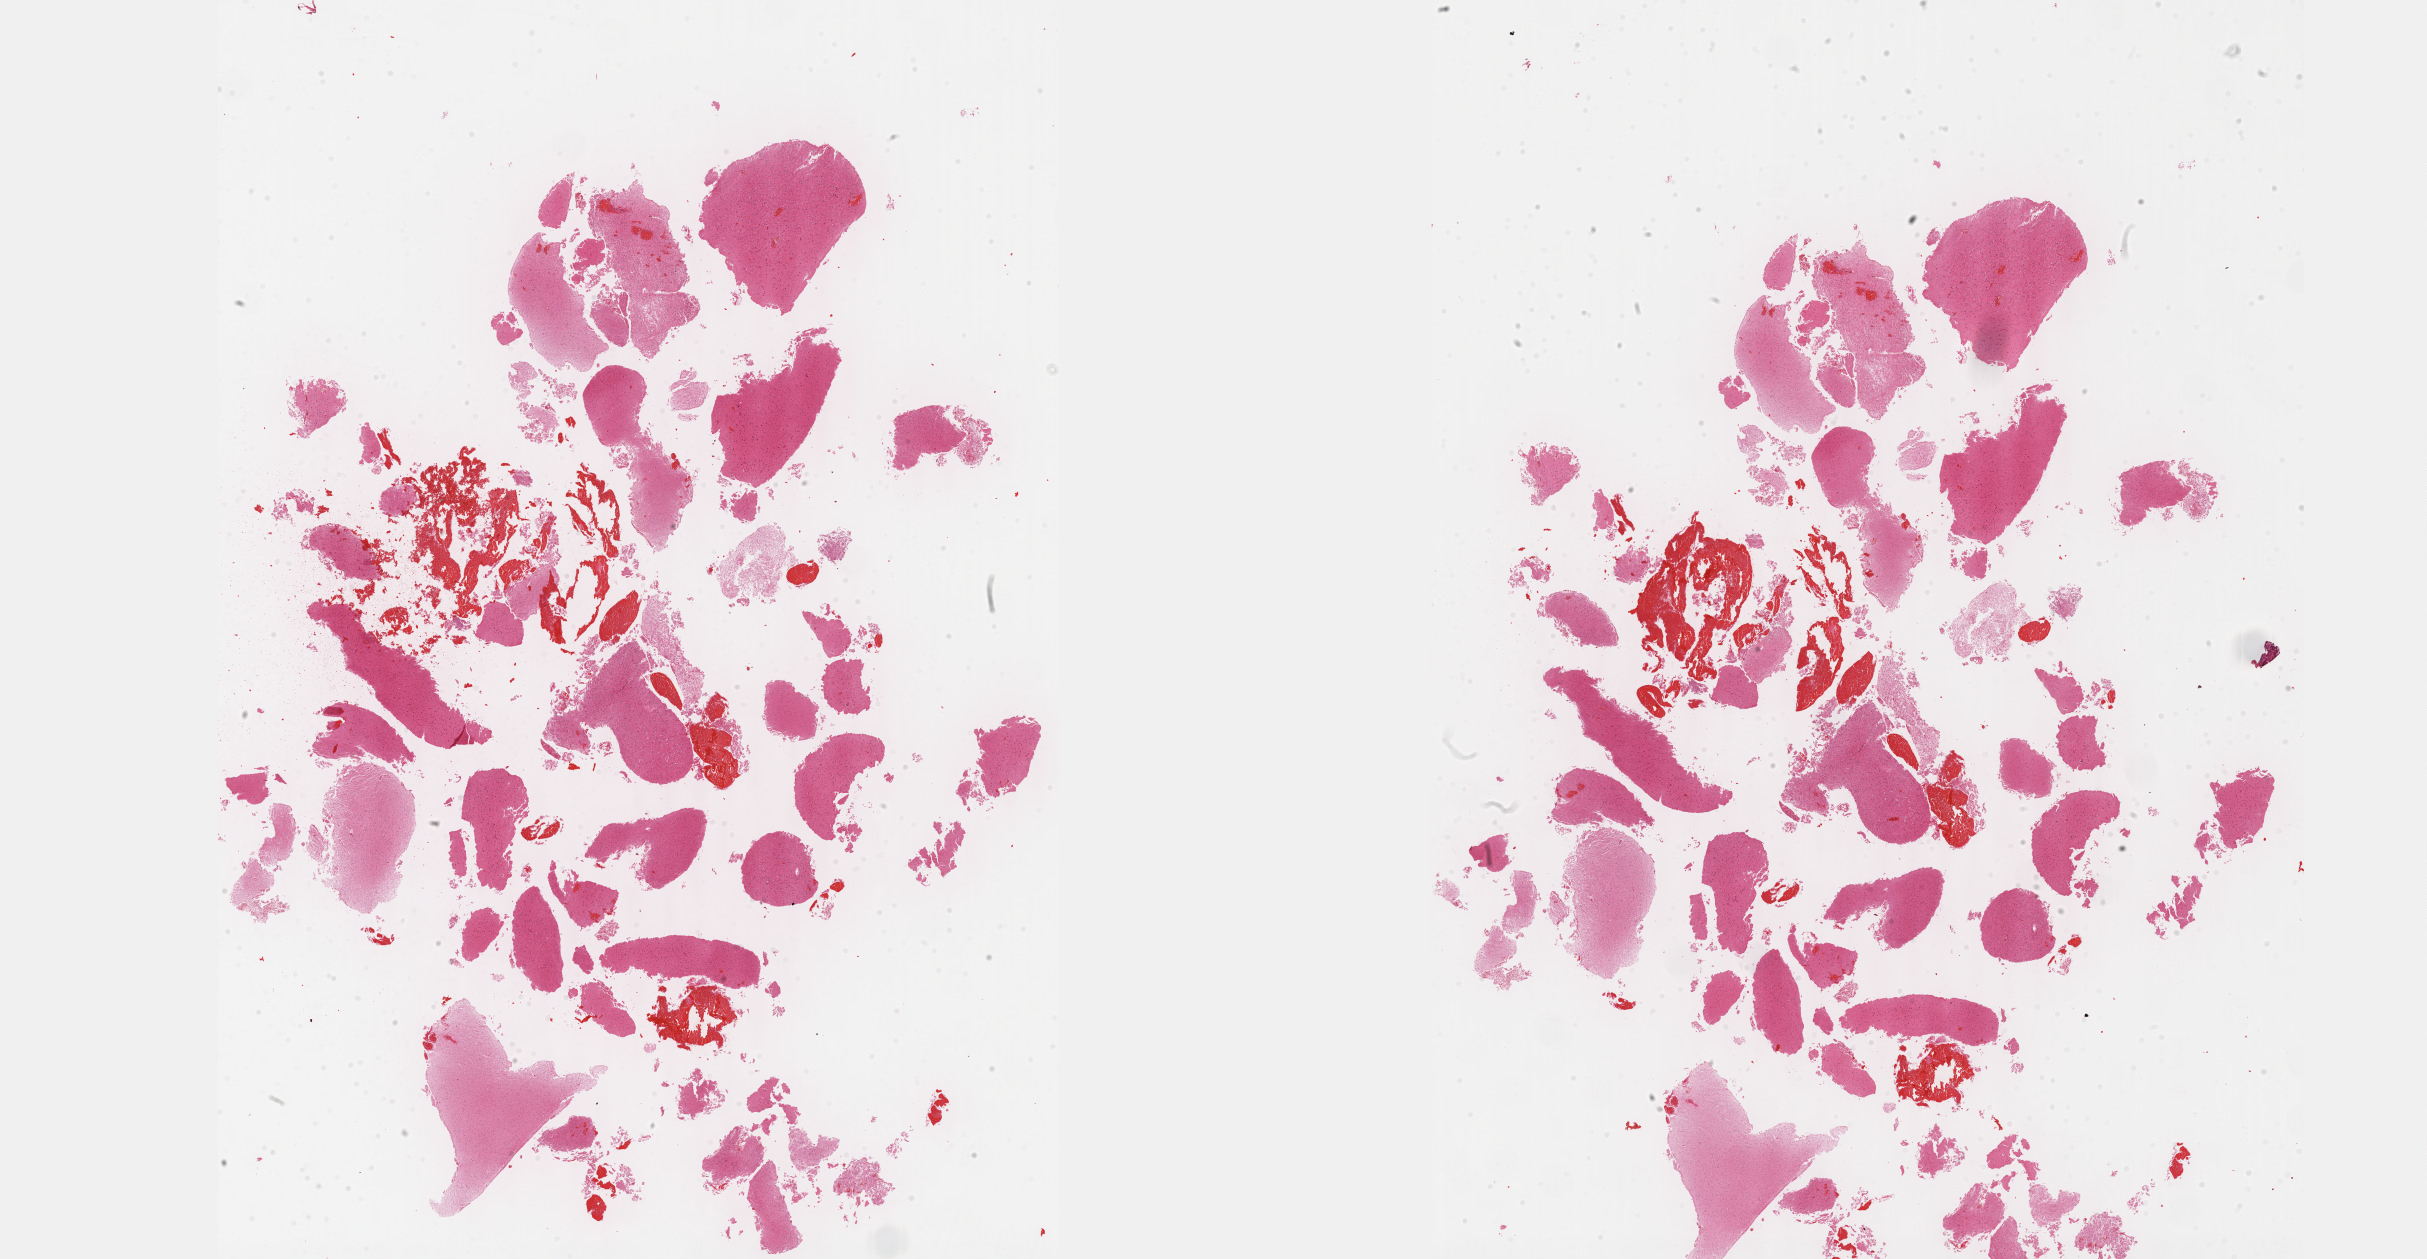
H&E whole-slide image, a low-resolution overview of the entire scanned area, about 39.2 x 20.4 mm, FFPE section, primary tumour sample from the brain. Male, age 44 years at initial diagnosis. Histologic grade: G2 (moderately differentiated).
Histologic diagnosis: Astrocytoma, NOS (cerebrum).